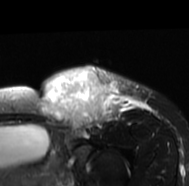
MRI of an extremity soft-tissue mass, one axial slice; T2-weighted fat-saturated; MR volume resampled by the dataset authors to the PET/CT grid (not the native acquisition matrix); 189 × 186 image matrix. Female patient. Case-level facts recorded for this patient, not image findings: histological type: leiomyosarcoma; grade: high; site of the primary tumour: groin.
Annotated regions visible in this slice (expert contour drawn on MRI and transferred to this co-registered scan by the dataset authors):
- gross tumour volume including surrounding oedema: box from (x=38, y=65) to (x=151, y=140) px
- gross tumour volume (mass): (x=38, y=66)–(x=112, y=128)